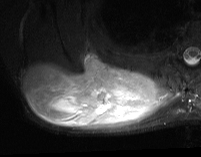
MRI of an extremity soft-tissue mass, one axial slice; position 30 of 74 along the scan axis; STIR; MR volume resampled by the dataset authors to the PET/CT grid (not the native acquisition matrix); 3.27 mm slice thickness; 201 × 157 image matrix, field of view 196 × 153 mm. Male patient. Case-level facts recorded for this patient, not image findings: histological type: pleiomorphic spindle cell undifferentiated; grade: high; site of the primary tumour: right parascapusular.
Annotated regions visible in this slice (expert contour drawn on MRI and transferred to this co-registered scan by the dataset authors):
- gross tumour volume including surrounding oedema: bounding box [x1, y1, x2, y2] px = [24, 52, 175, 131]
- gross tumour volume (mass): [24, 52, 157, 127]